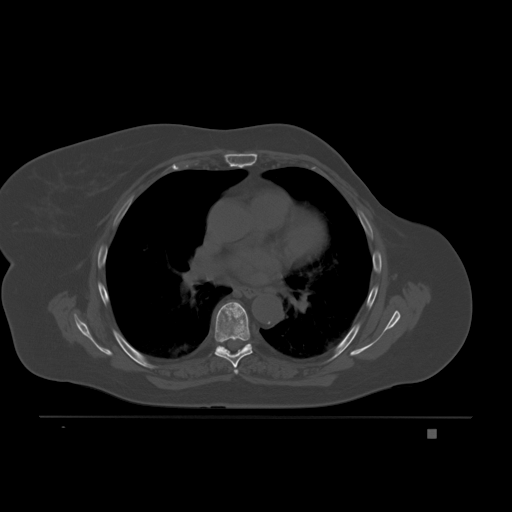
CT including the spine, one axial slice; position 135 of 221 along the scan axis; bone window (W 1800 / L 400 HU); 512 × 512 image matrix, field of view 474 × 474 mm. Patient: female, 63 years. Case-level facts recorded for this patient, not image findings: primary cancer: breast.
Structures marked on this image (semi-automatic segmentation, software-assisted and operator-edited):
- T5 vertebra: bounding box (x1, y1, x2, y2) in pixels: (234, 369, 238, 374)
- T6 vertebra: (214, 302, 253, 371)
- T7 vertebra: (217, 344, 248, 351)